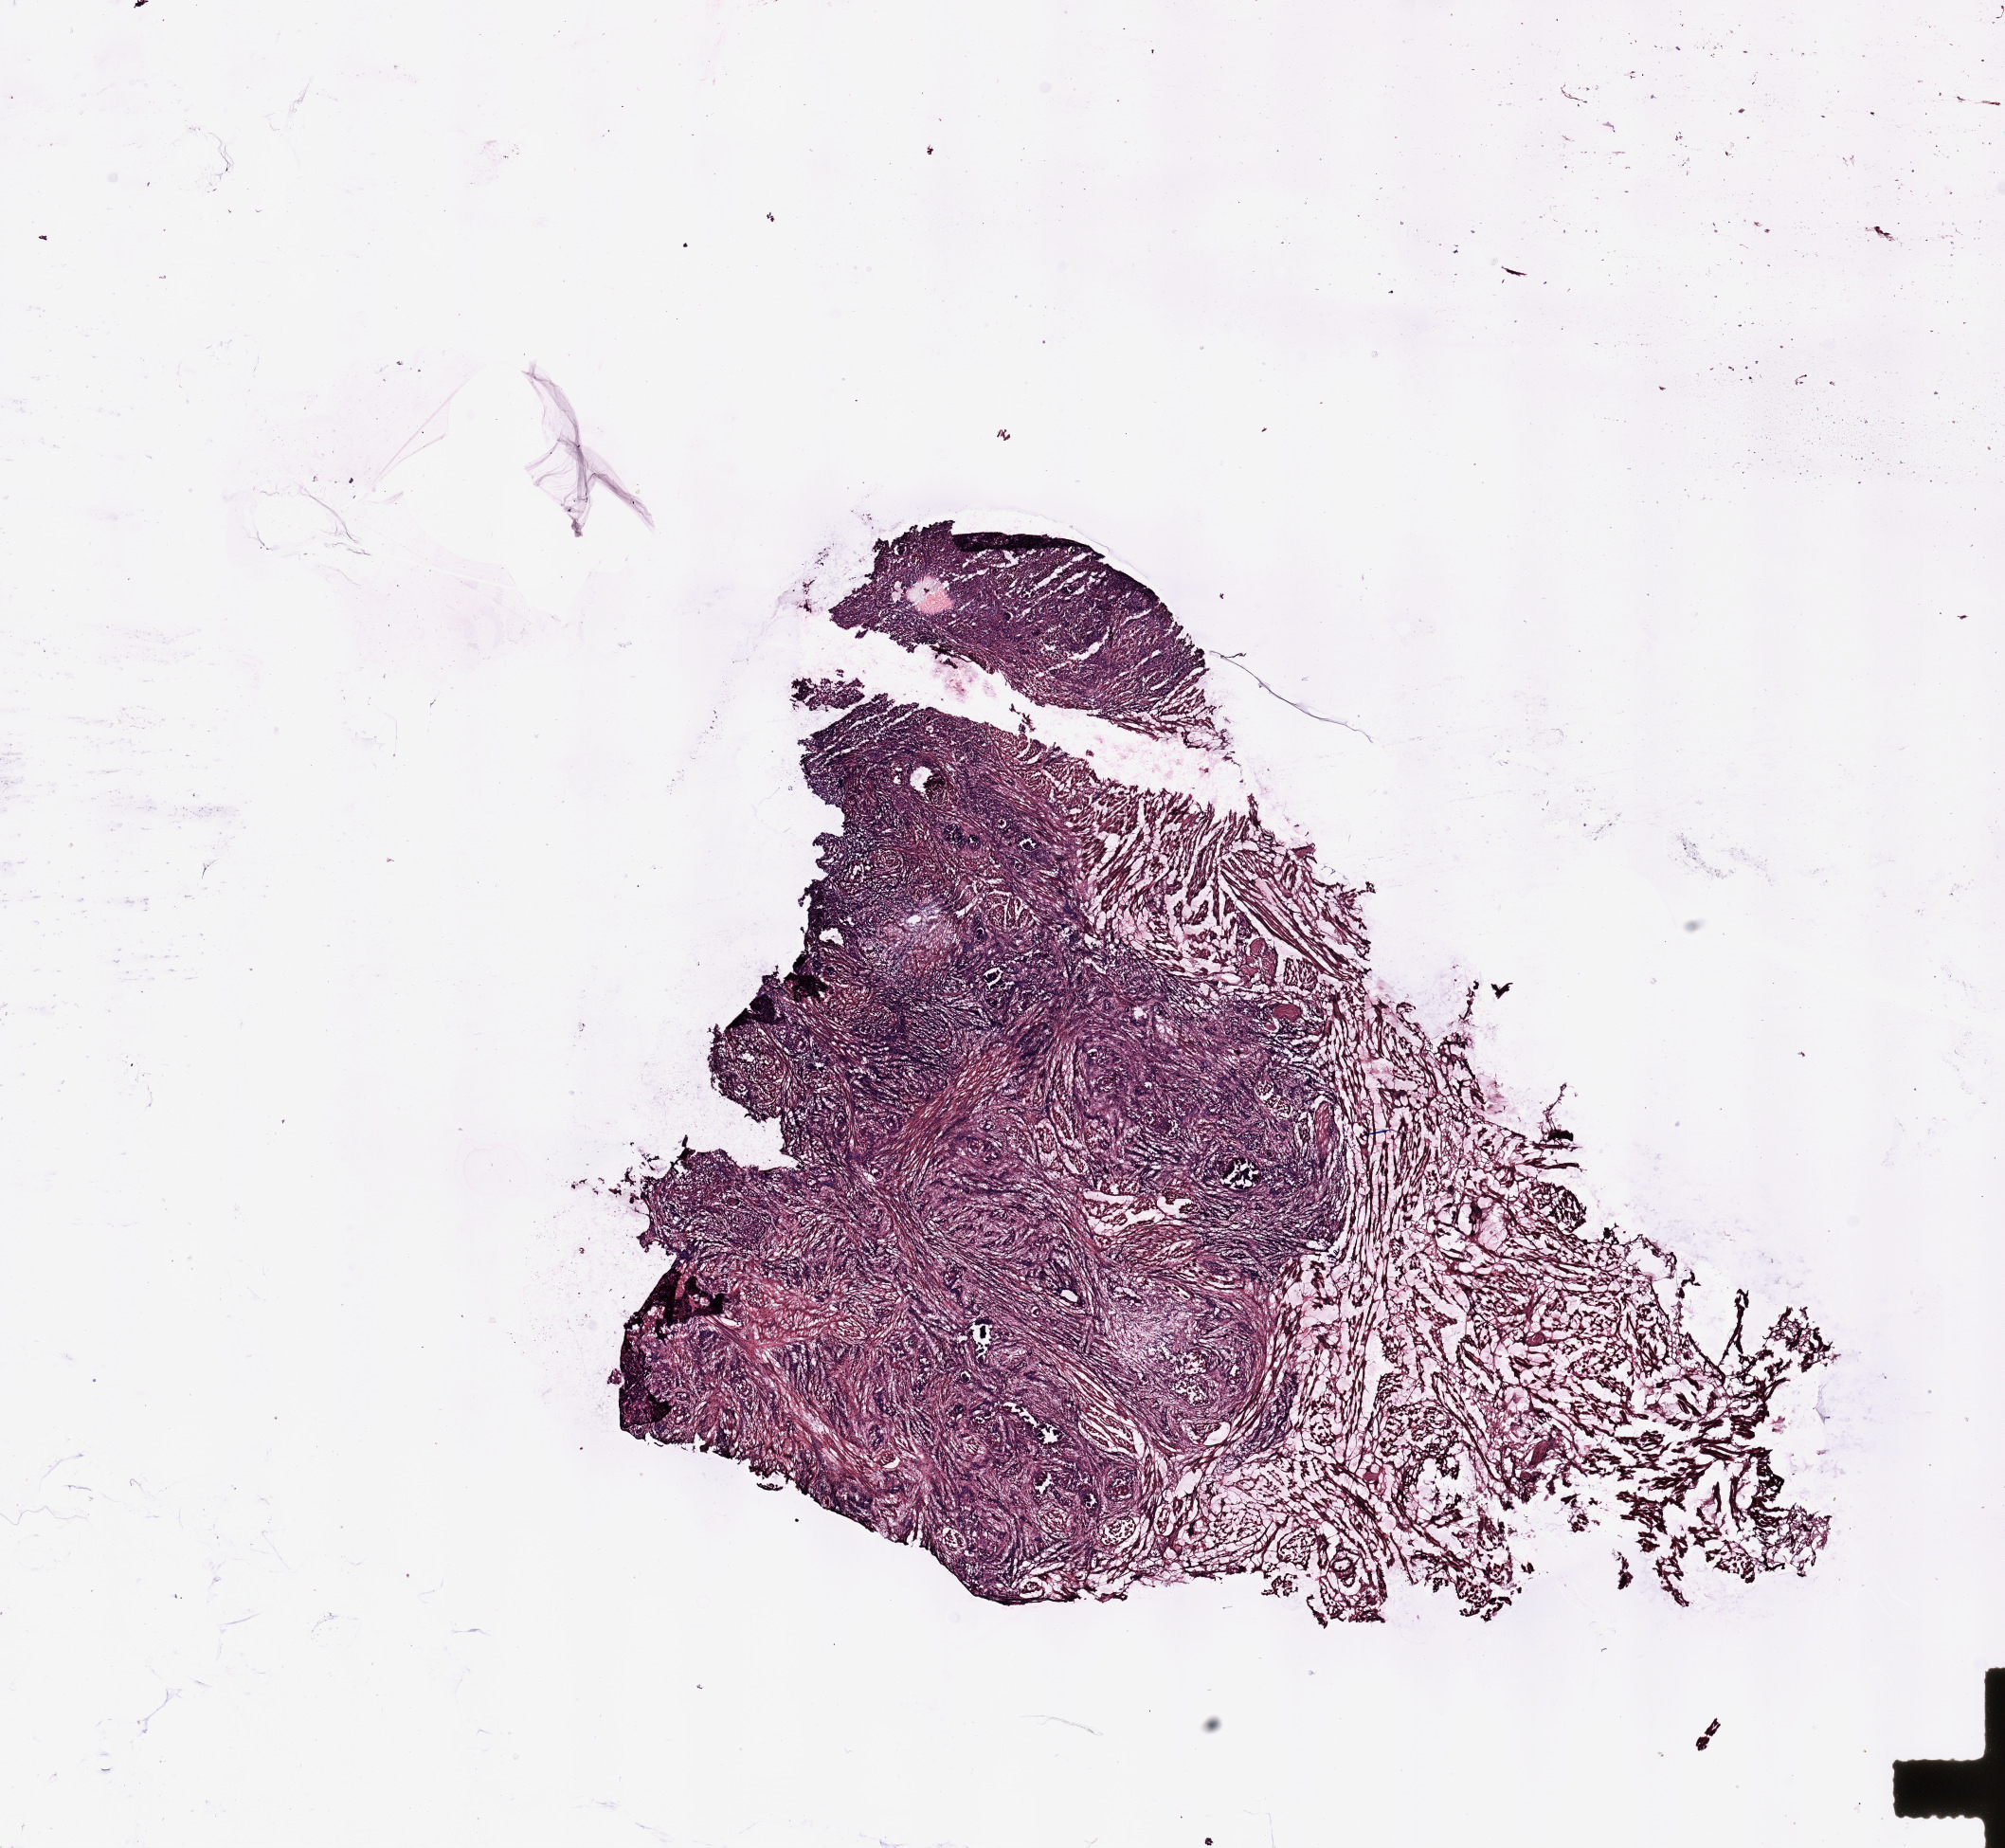
Whole-slide histology image, Hematoxylin and eosin (H&E) stained — low-resolution overview of the scanned area, about 16.7 x 15.4 mm (slide scanned at 20x), head and neck, tissue type not recorded. Male, 67 y/o.
Patient diagnosis: Squamous cell carcinoma, NOS.